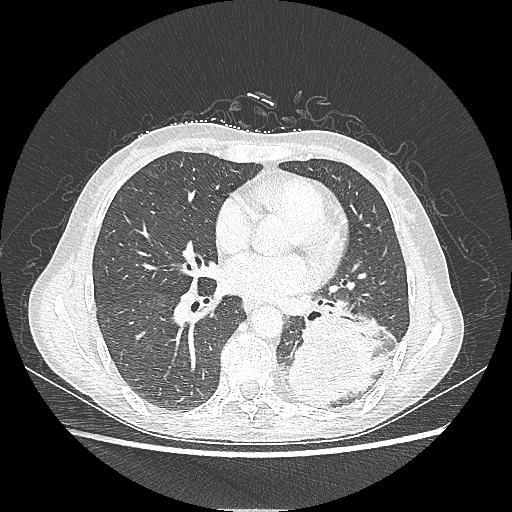
Chest CT, one axial slice; position 104 of 220 along the scan axis; lung window (W 1500 / L -600 HU); 512 × 512 image matrix. Patient: female, 53 years. From the clinical record (not read from this slice): clinical TNM (as recorded): T3 N0 M0.
Annotated regions visible in this slice (rectangle marked by the reading radiologist):
- lung tumour (recorded histology: adenocarcinoma): bounding box (x1, y1, x2, y2) in pixels: (284, 311, 398, 408)